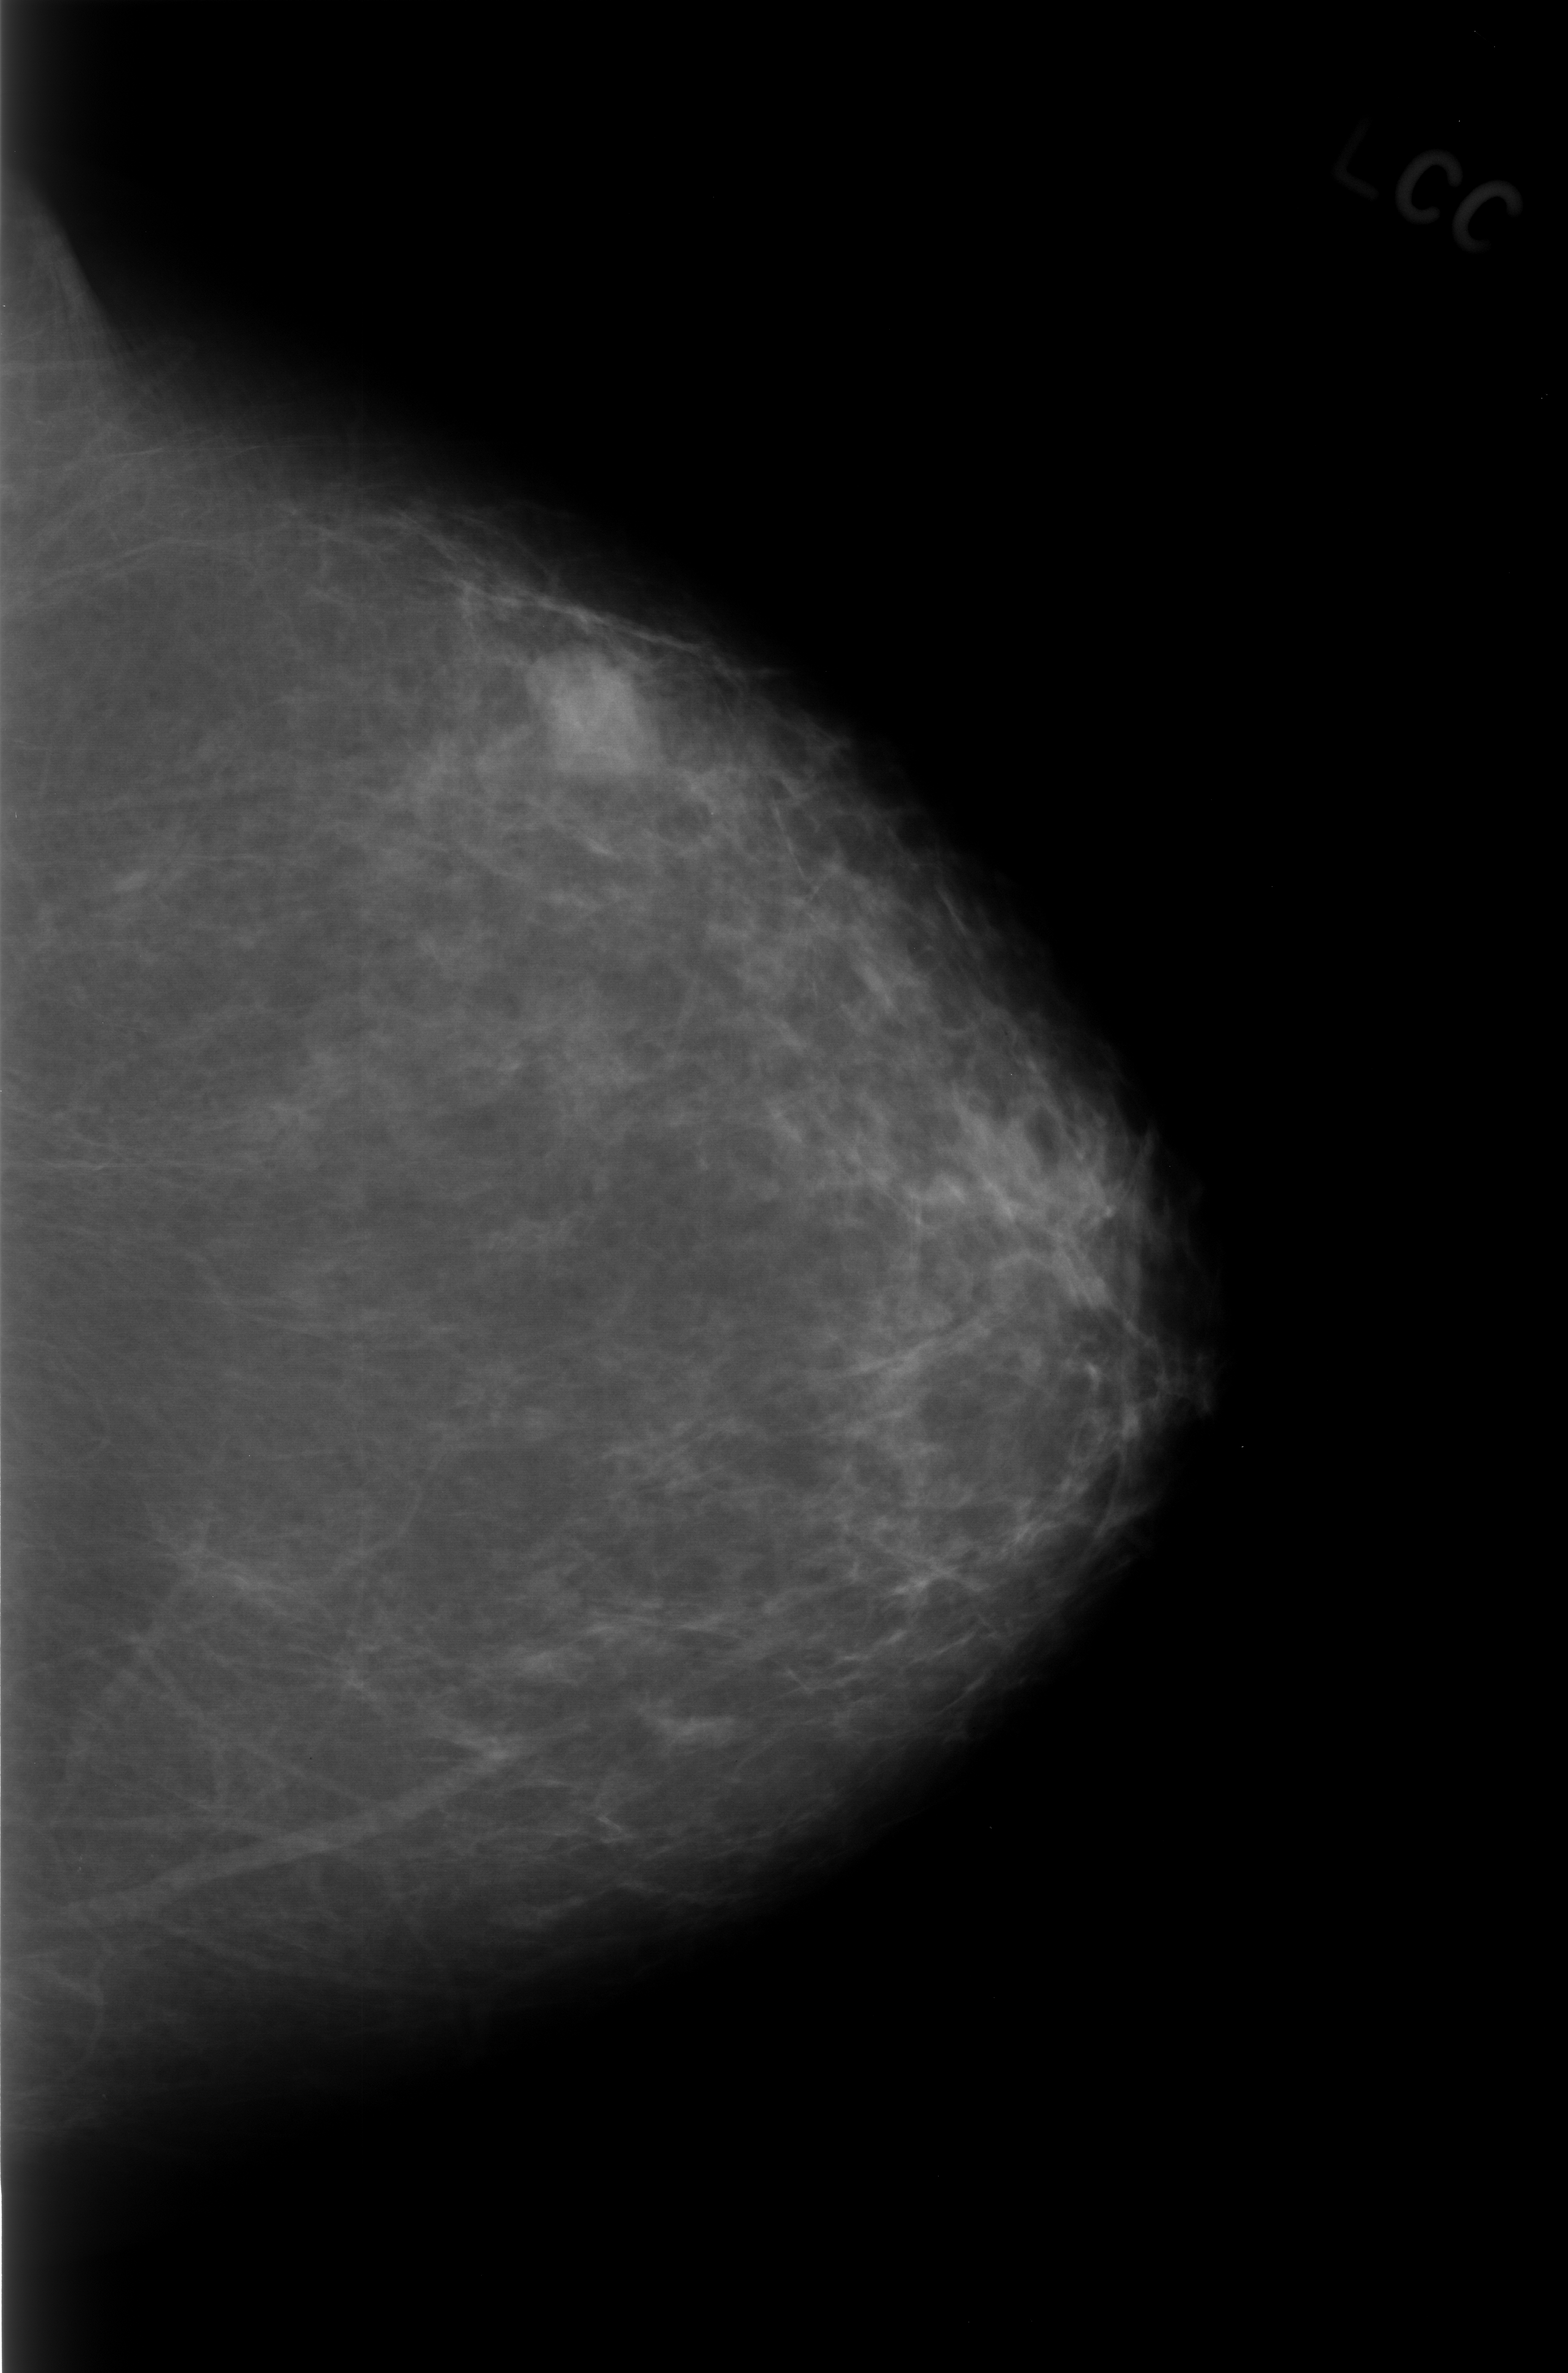
Digitized screen-film mammogram; left breast; craniocaudal (CC) view; breast composition: almost entirely fatty (BI-RADS density category 1 of 4); 1568 × 2373 image matrix.
Marked abnormalities (boxes around the expert regions of interest):
- mass, shape lobulated, margins obscured; BI-RADS assessment category 3; subtlety rating 5 on a 1 (subtle) to 5 (obvious) scale; pathology (as recorded): benign: box from (x=523, y=643) to (x=668, y=783) px